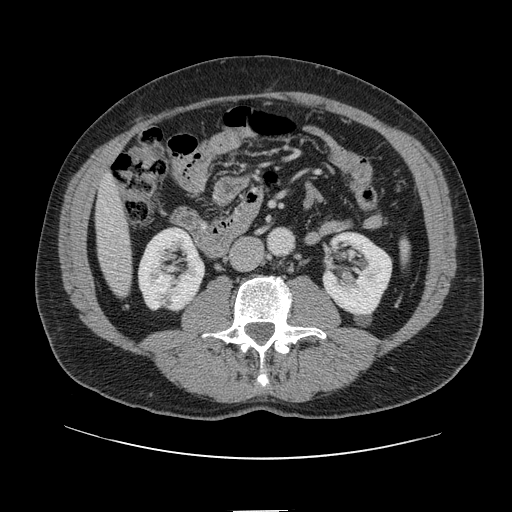
Contrast-enhanced abdominal CT, one axial slice; position 19 of 161 along the scan axis; 120 kVp; intravenous contrast given; soft-tissue window (W 400 / L 40 HU); 2.5 mm slice thickness; 512 × 512 image matrix, field of view 412 × 412 mm. Male patient, age 66 years. Case-level facts recorded for this patient, not image findings: diagnosis: colorectal cancer liver metastases, imaged before liver resection.
Outlined on this slice (expert manual segmentation):
- liver: bounding box [x1, y1, x2, y2] px = [96, 180, 131, 295]
- planned liver remnant (the part of the liver to remain after resection): [96, 179, 126, 250]